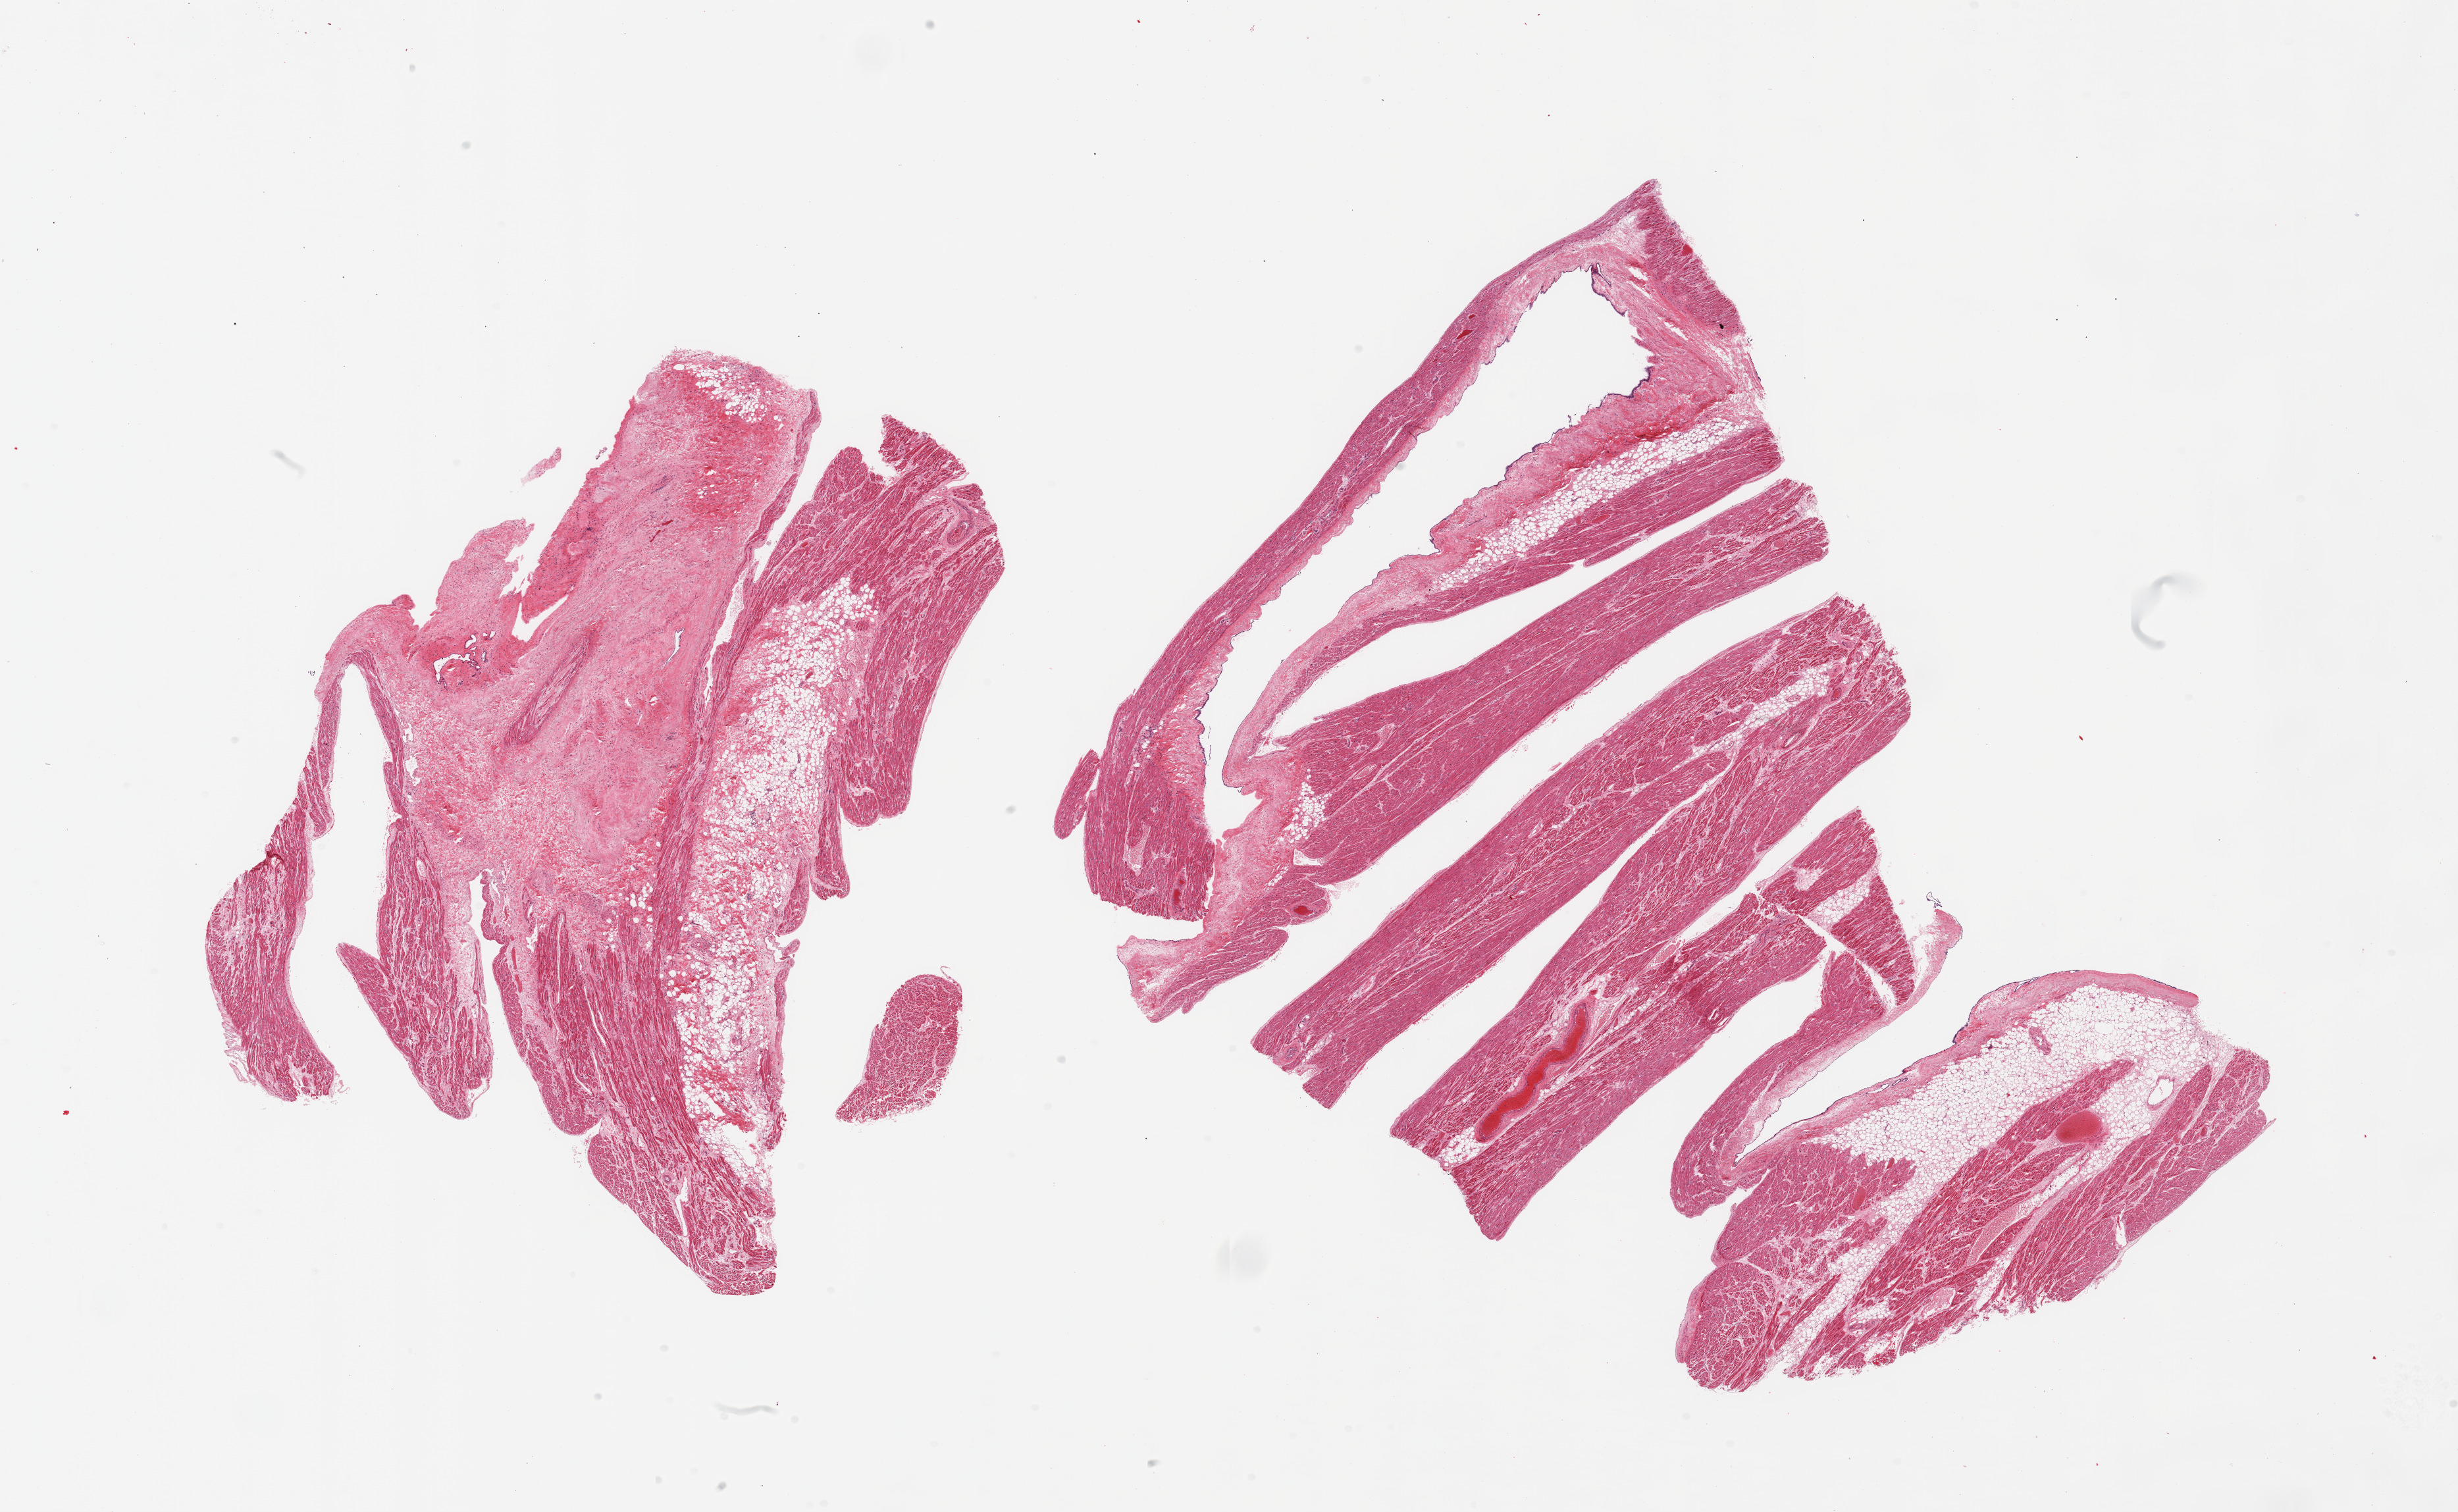
Hematoxylin and eosin (H&E) whole-slide image, brightfield, a low-resolution overview of the entire scanned area, about 29.5 x 18.2 mm (from a 20x scan). PAXgene-fixed paraffin-embedded (PFPE) section. Target tissue: auricular appendage. Donor tissue sample. Donor sex: male.
Reviewer comment on this tissue sample: 2 pieces; 1 piece is ~30% fibrous/~20% internal fat, 2nd also includes ~20% fat.